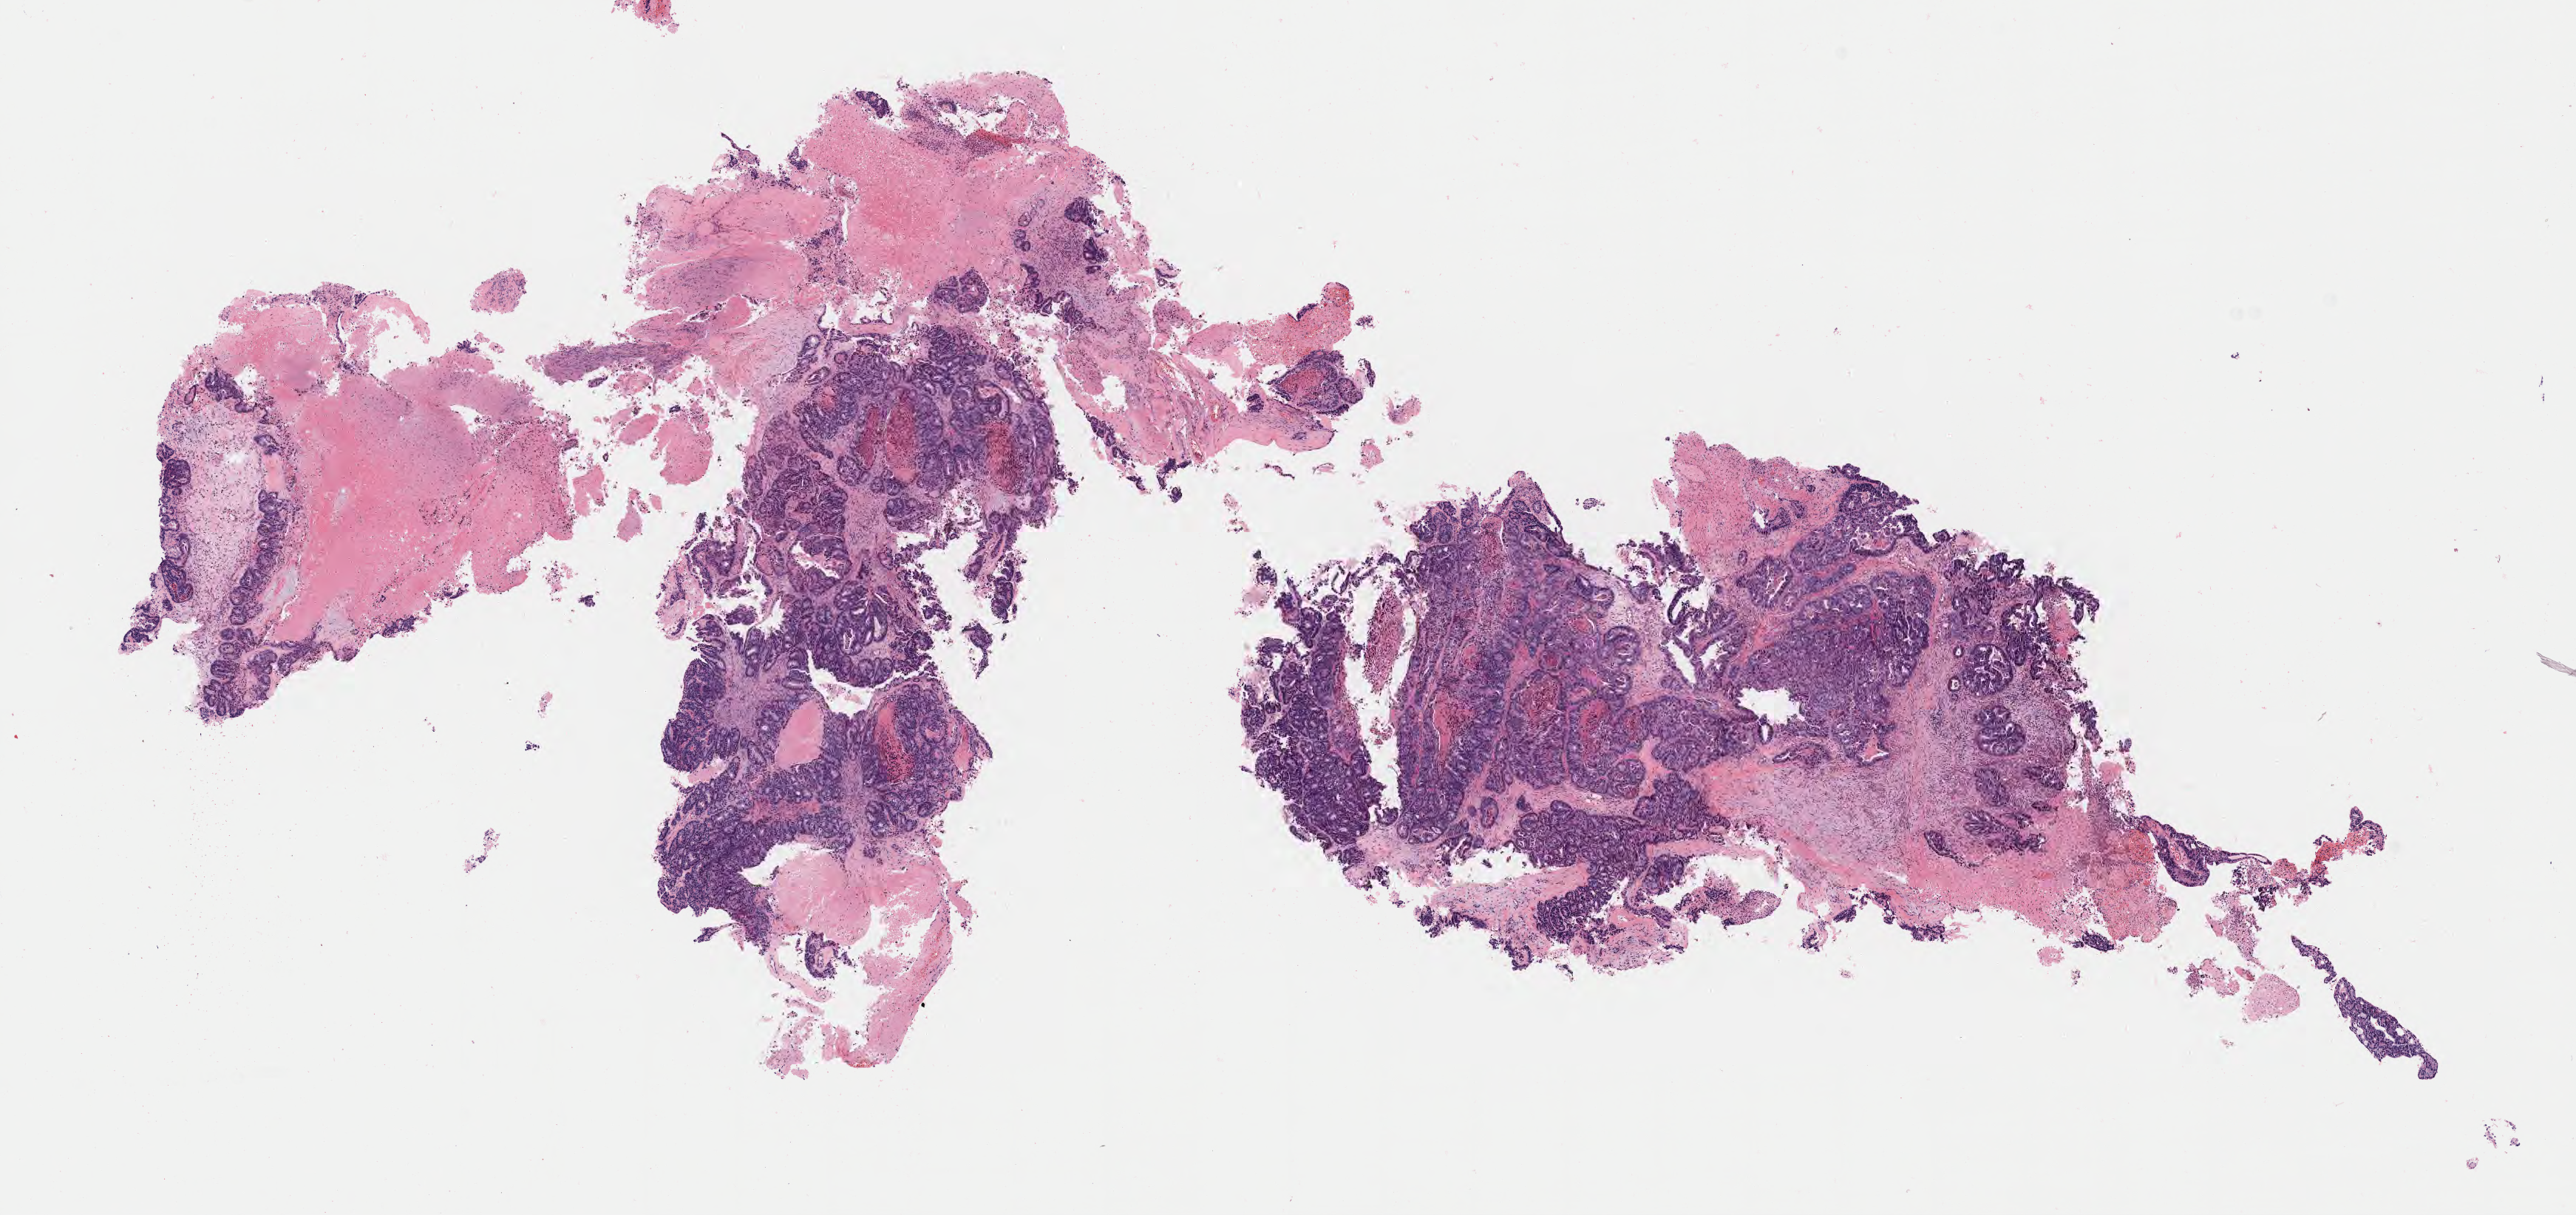
Digitized H&E-stained section, a low-resolution overview of the entire scanned area, about 14.1 x 6.6 mm. Specimen: tumor tissue. Anatomic site: cervix. Patient female; aged 48.
Diagnosis: Adenocarcinoma, NOS.